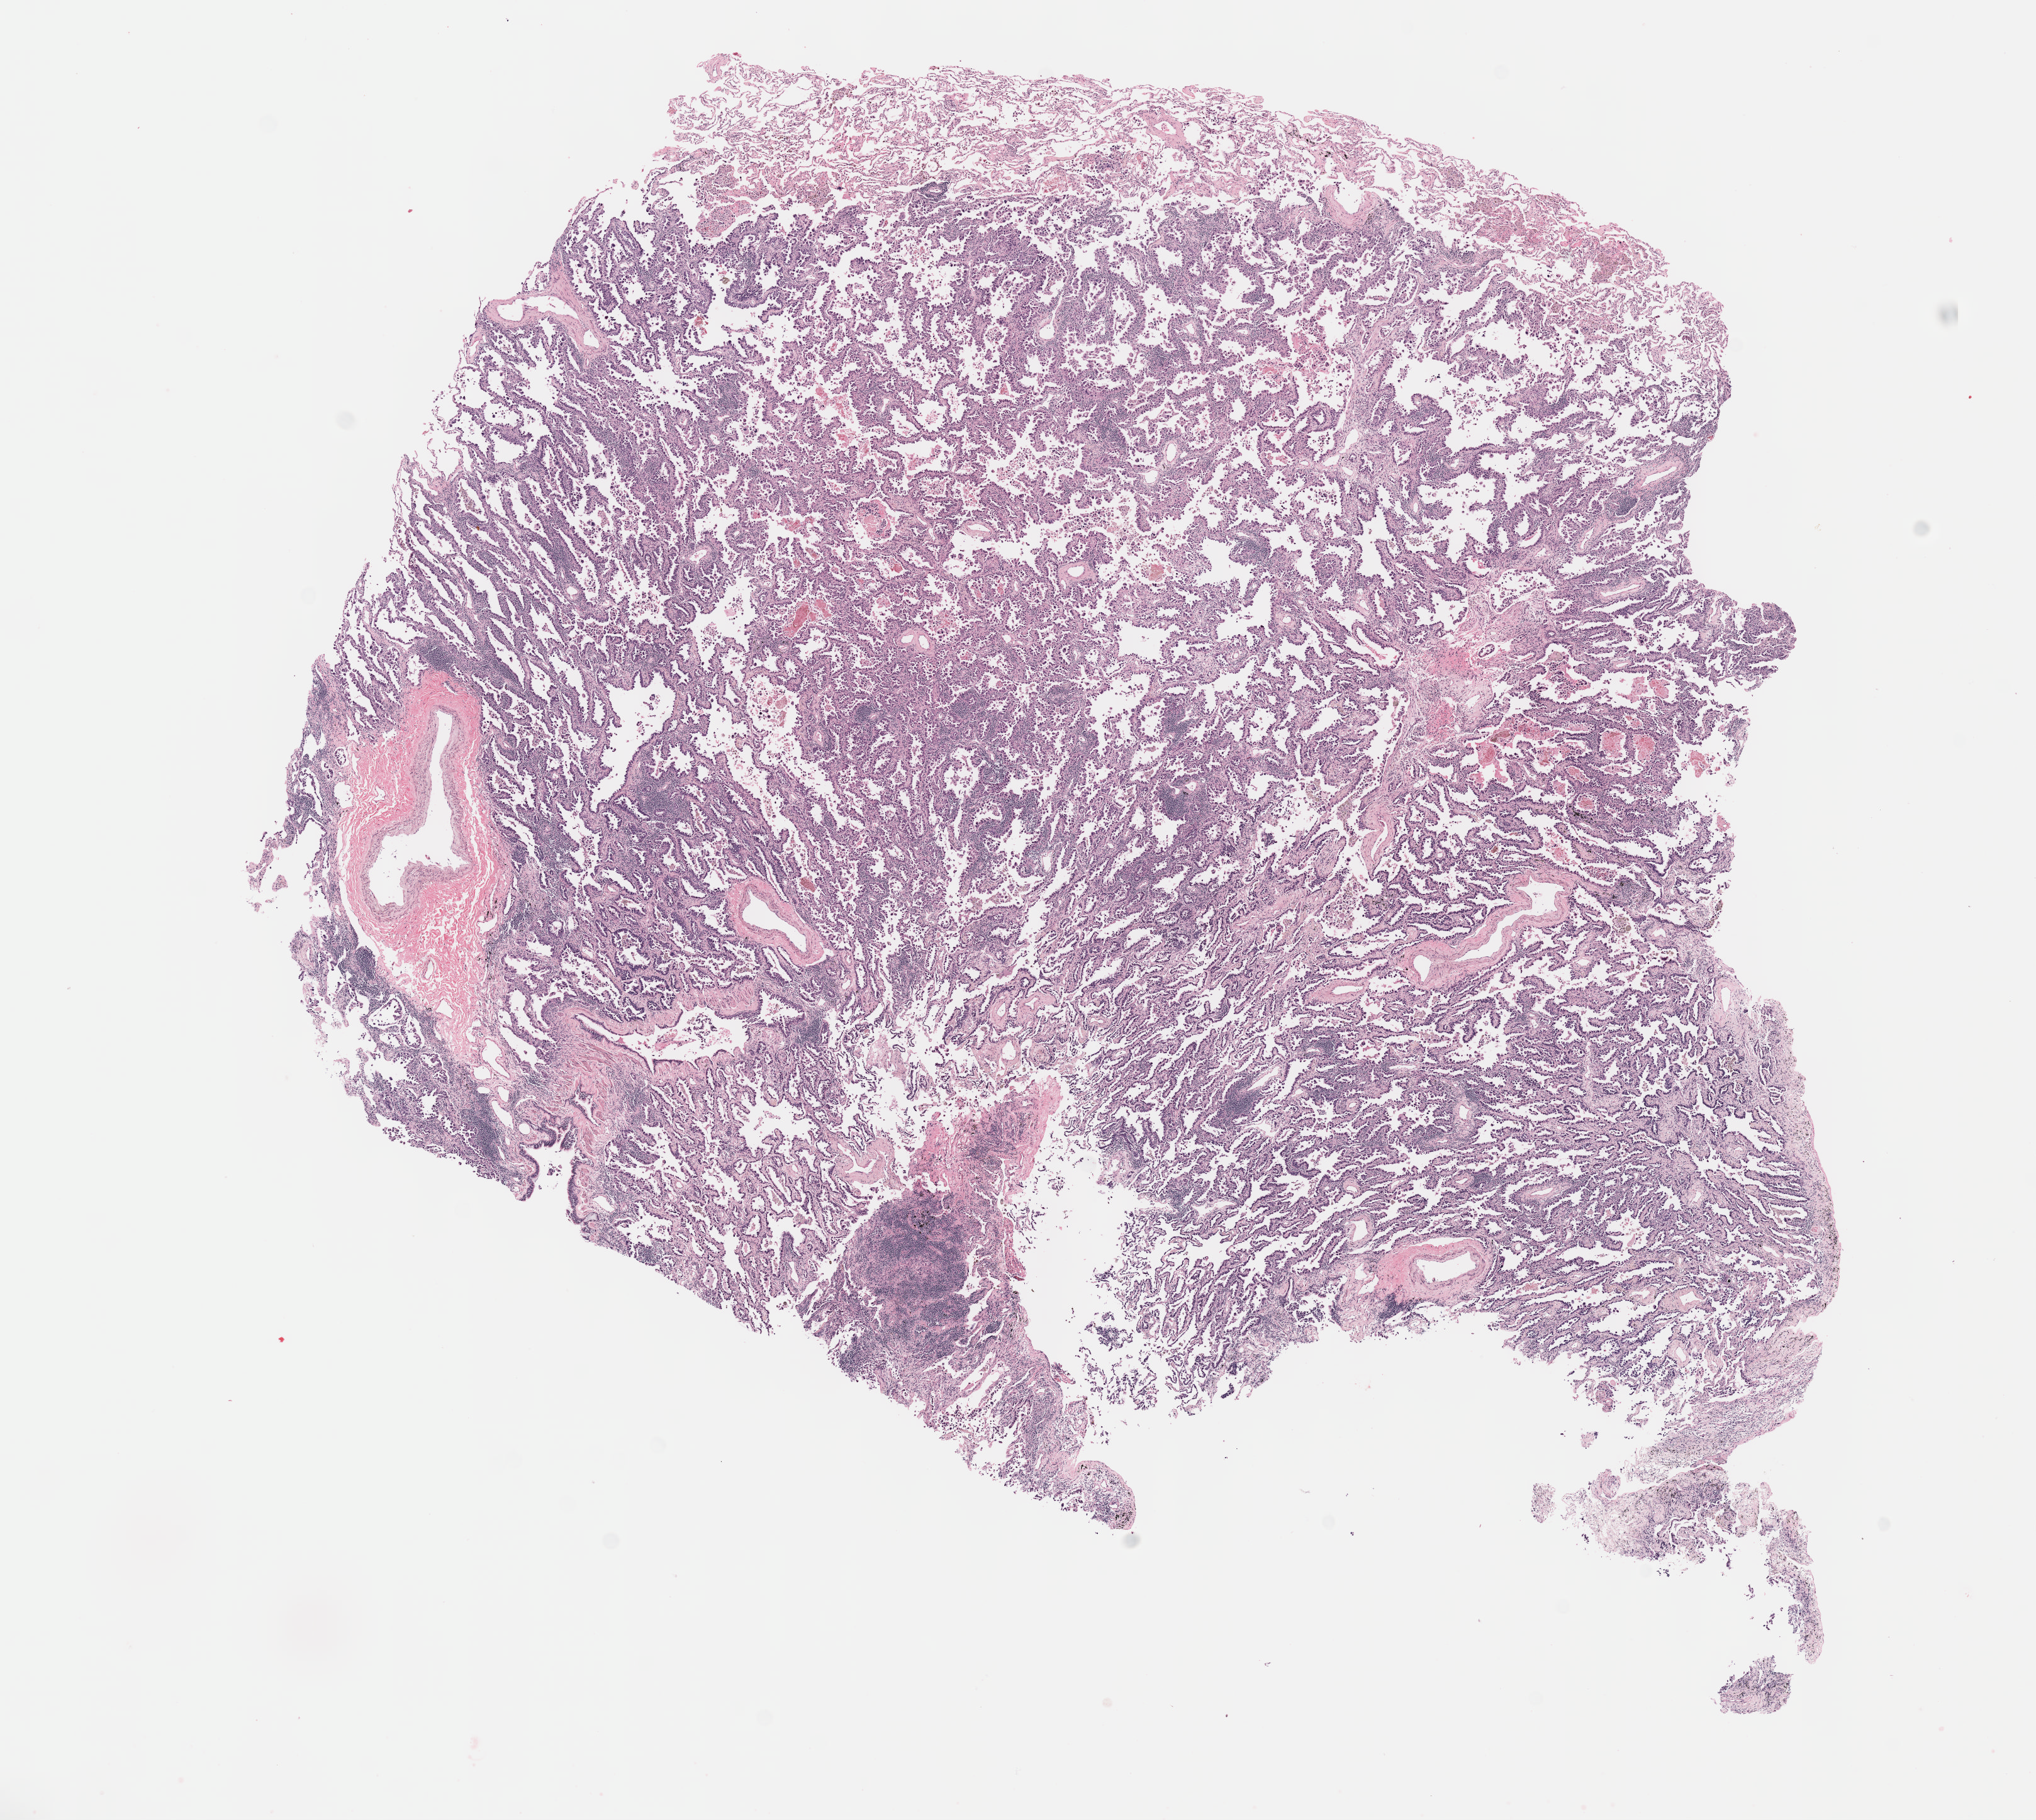
H&E-stained whole-slide image — a low-resolution overview of the entire scanned area, about 13.1 x 11.7 mm. FFPE section. Lung, primary tumour sample. Male, age 60 years at initial diagnosis.
Histologic diagnosis: Bronchiolo-alveolar carcinoma, non-mucinous (upper lobe, lung). AJCC pathologic stage: IB. Laterality: right.